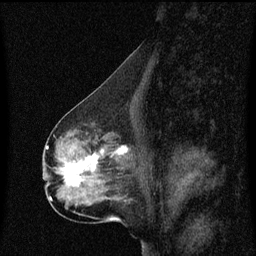
Breast MRI (dynamic contrast-enhanced), one sagittal slice. Position 29 of 60 along the scan axis. Dynamic contrast-enhanced series, image 2 of 3 at this slice position (ordered by acquisition). 1.5 T. TE 4.2 ms, TR 8.4 ms. 2 mm slice thickness. 256 × 256 image matrix, field of view 200 × 200 mm. Female patient, age 50 years. From the clinical record (not read from this slice): setting: breast cancer imaged before/during neoadjuvant chemotherapy; receptor status: HR-positive, HER2-negative.
Structures marked on this image (semi-automatic segmentation, software-assisted and operator-edited):
- analysis volume of interest (the breast-tissue region the enhancement analysis was run in; not a lesion): bounding box [x1, y1, x2, y2] px = [55, 140, 133, 191]
- tumour enhancement mask (voxels above the 70 % enhancement threshold inside the analysis volume of interest): [61, 148, 128, 187]